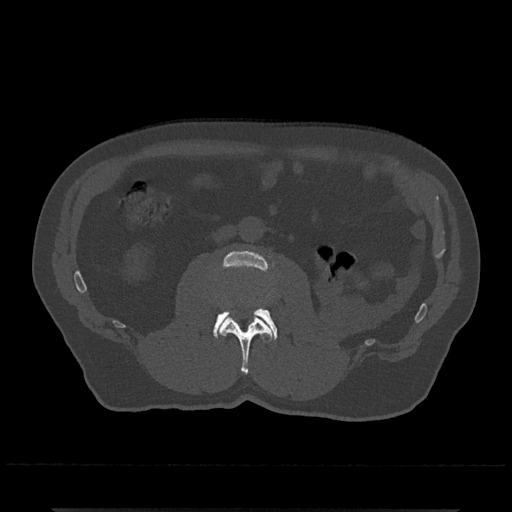
CT including the spine, one axial slice; position 262 of 797 along the scan axis; reconstruction kernel Br40s/3; 120 kVp; bone window (W 1800 / L 400 HU); 512 × 512 image matrix. Patient: male, 67 years. From the clinical record (not read from this slice): primary cancer: prostate.
Annotated regions visible in this slice (semi-automatic segmentation, software-assisted and operator-edited):
- L2 vertebra: bounding box [x1, y1, x2, y2] px = [219, 315, 273, 374]
- L3 vertebra: [213, 251, 278, 340]